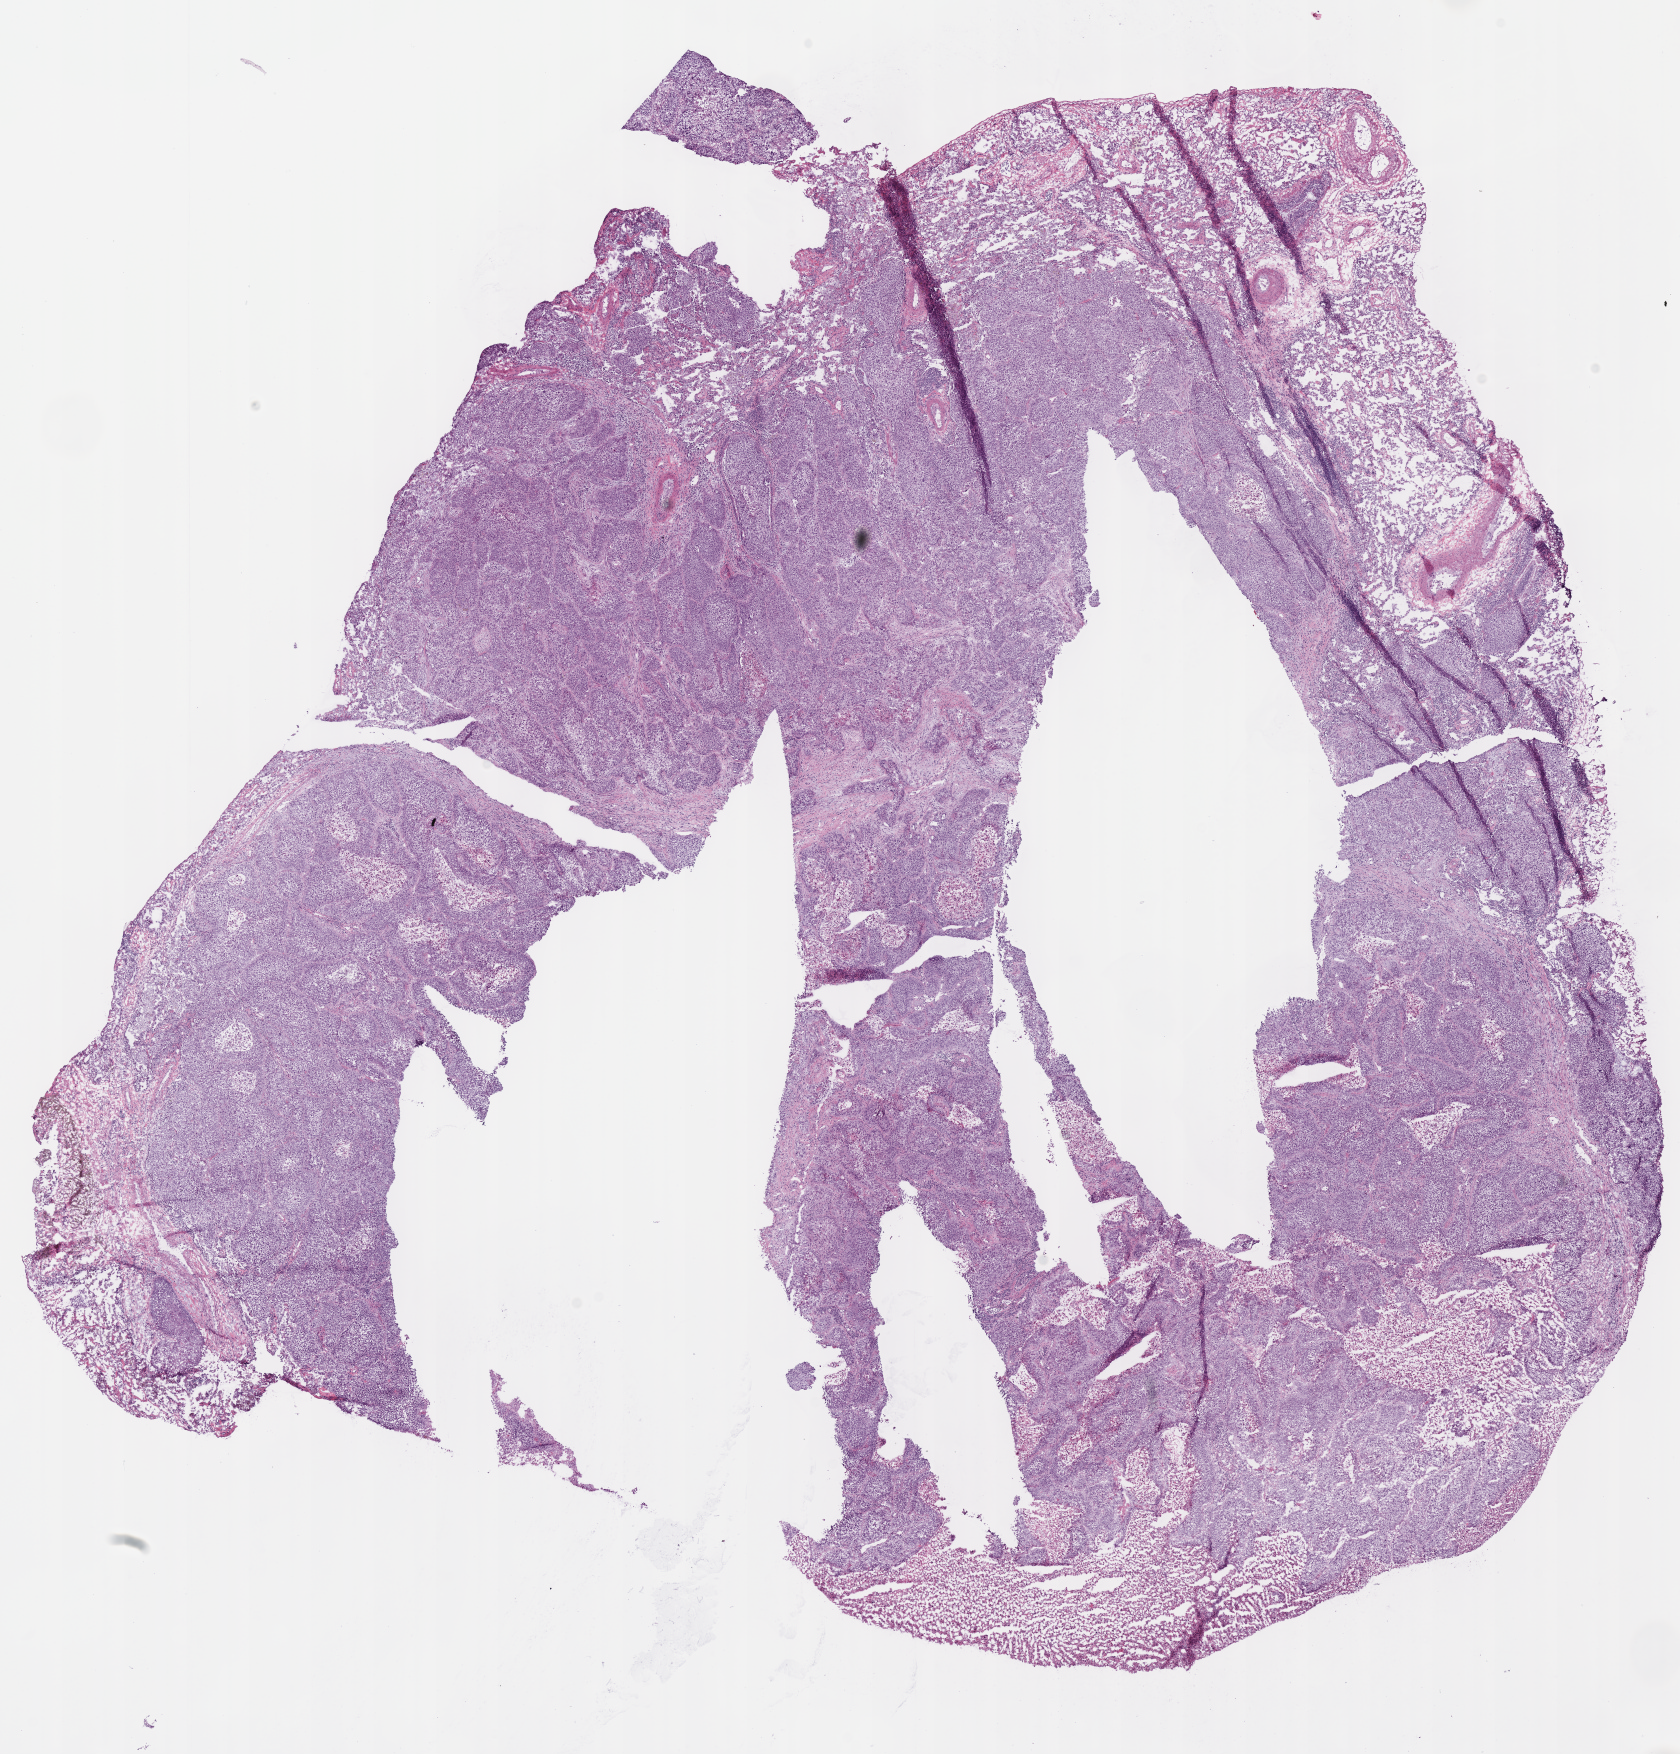
Whole-slide histology image, Hematoxylin and eosin (H&E) stained, shown as a low-resolution overview of the whole scanned area (about 13.2 x 13.8 mm, slide scanned at 40x). Frozen section. Sample: primary tumour, lung. Patient: female, age at initial diagnosis 59 years. Slide review estimates, as recorded: tumour cells 86%, tumour nuclei 80%, normal cells 12%, stromal cells 0%, necrosis 2%. Infiltration values recorded for this section: lymphocyte infiltration 5%, monocyte infiltration 7%.
• AJCC pathologic stage: IA
• laterality: left
• diagnosis: Squamous cell carcinoma, NOS (upper lobe, lung)